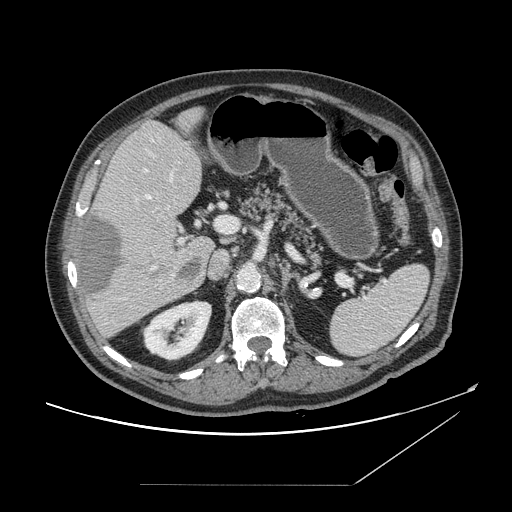
Contrast-enhanced abdominal CT, one axial slice; position 91 of 166 along the scan axis; 120 kVp; intravenous contrast given; soft-tissue window (W 400 / L 40 HU); 2.5 mm slice thickness; 512 × 512 image matrix, field of view 416 × 416 mm. Male patient, age 80 years. From the clinical record (not read from this slice): diagnosis: colorectal cancer liver metastases, imaged before liver resection; multiple liver metastases: no.
Annotated regions visible in this slice (manually delineated by an expert):
- hepatic veins: bounding box (x1, y1, x2, y2) in pixels: (144, 169, 173, 270)
- liver: (77, 109, 214, 337)
- planned liver remnant (the part of the liver to remain after resection): (97, 108, 214, 250)
- portal vein (with intrahepatic branches): (136, 198, 231, 244)
- liver metastasis: (85, 216, 201, 297)